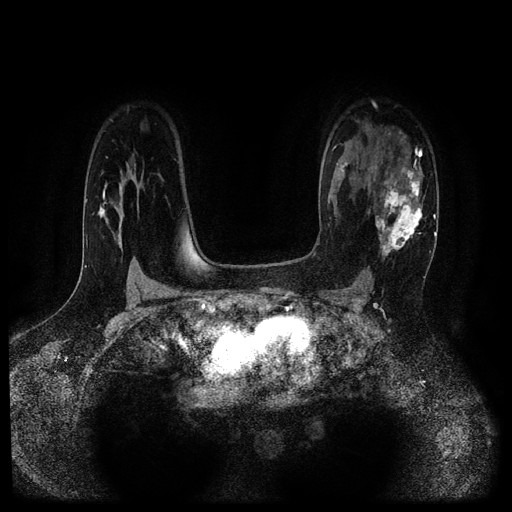
Breast MRI (dynamic contrast-enhanced, multi-phase), one axial slice. Slice 73 of 116 in the series (ordered by position). Dynamic contrast-enhanced series, time point 2 of 5 at this slice position (early post-contrast). 1.5 T. TE 2.7 ms, TR 5.4 ms. 2.2 mm slice thickness. 512 × 512 image matrix, field of view 330 × 330 mm. Female patient, age 43 years.
Structures marked on this image (semi-automatic segmentation, software-assisted and operator-edited):
- breast lesion (labelled 'tumour' in the annotation; benign lesions carry a separate 'benign' label): box from (x=373, y=166) to (x=424, y=263) px